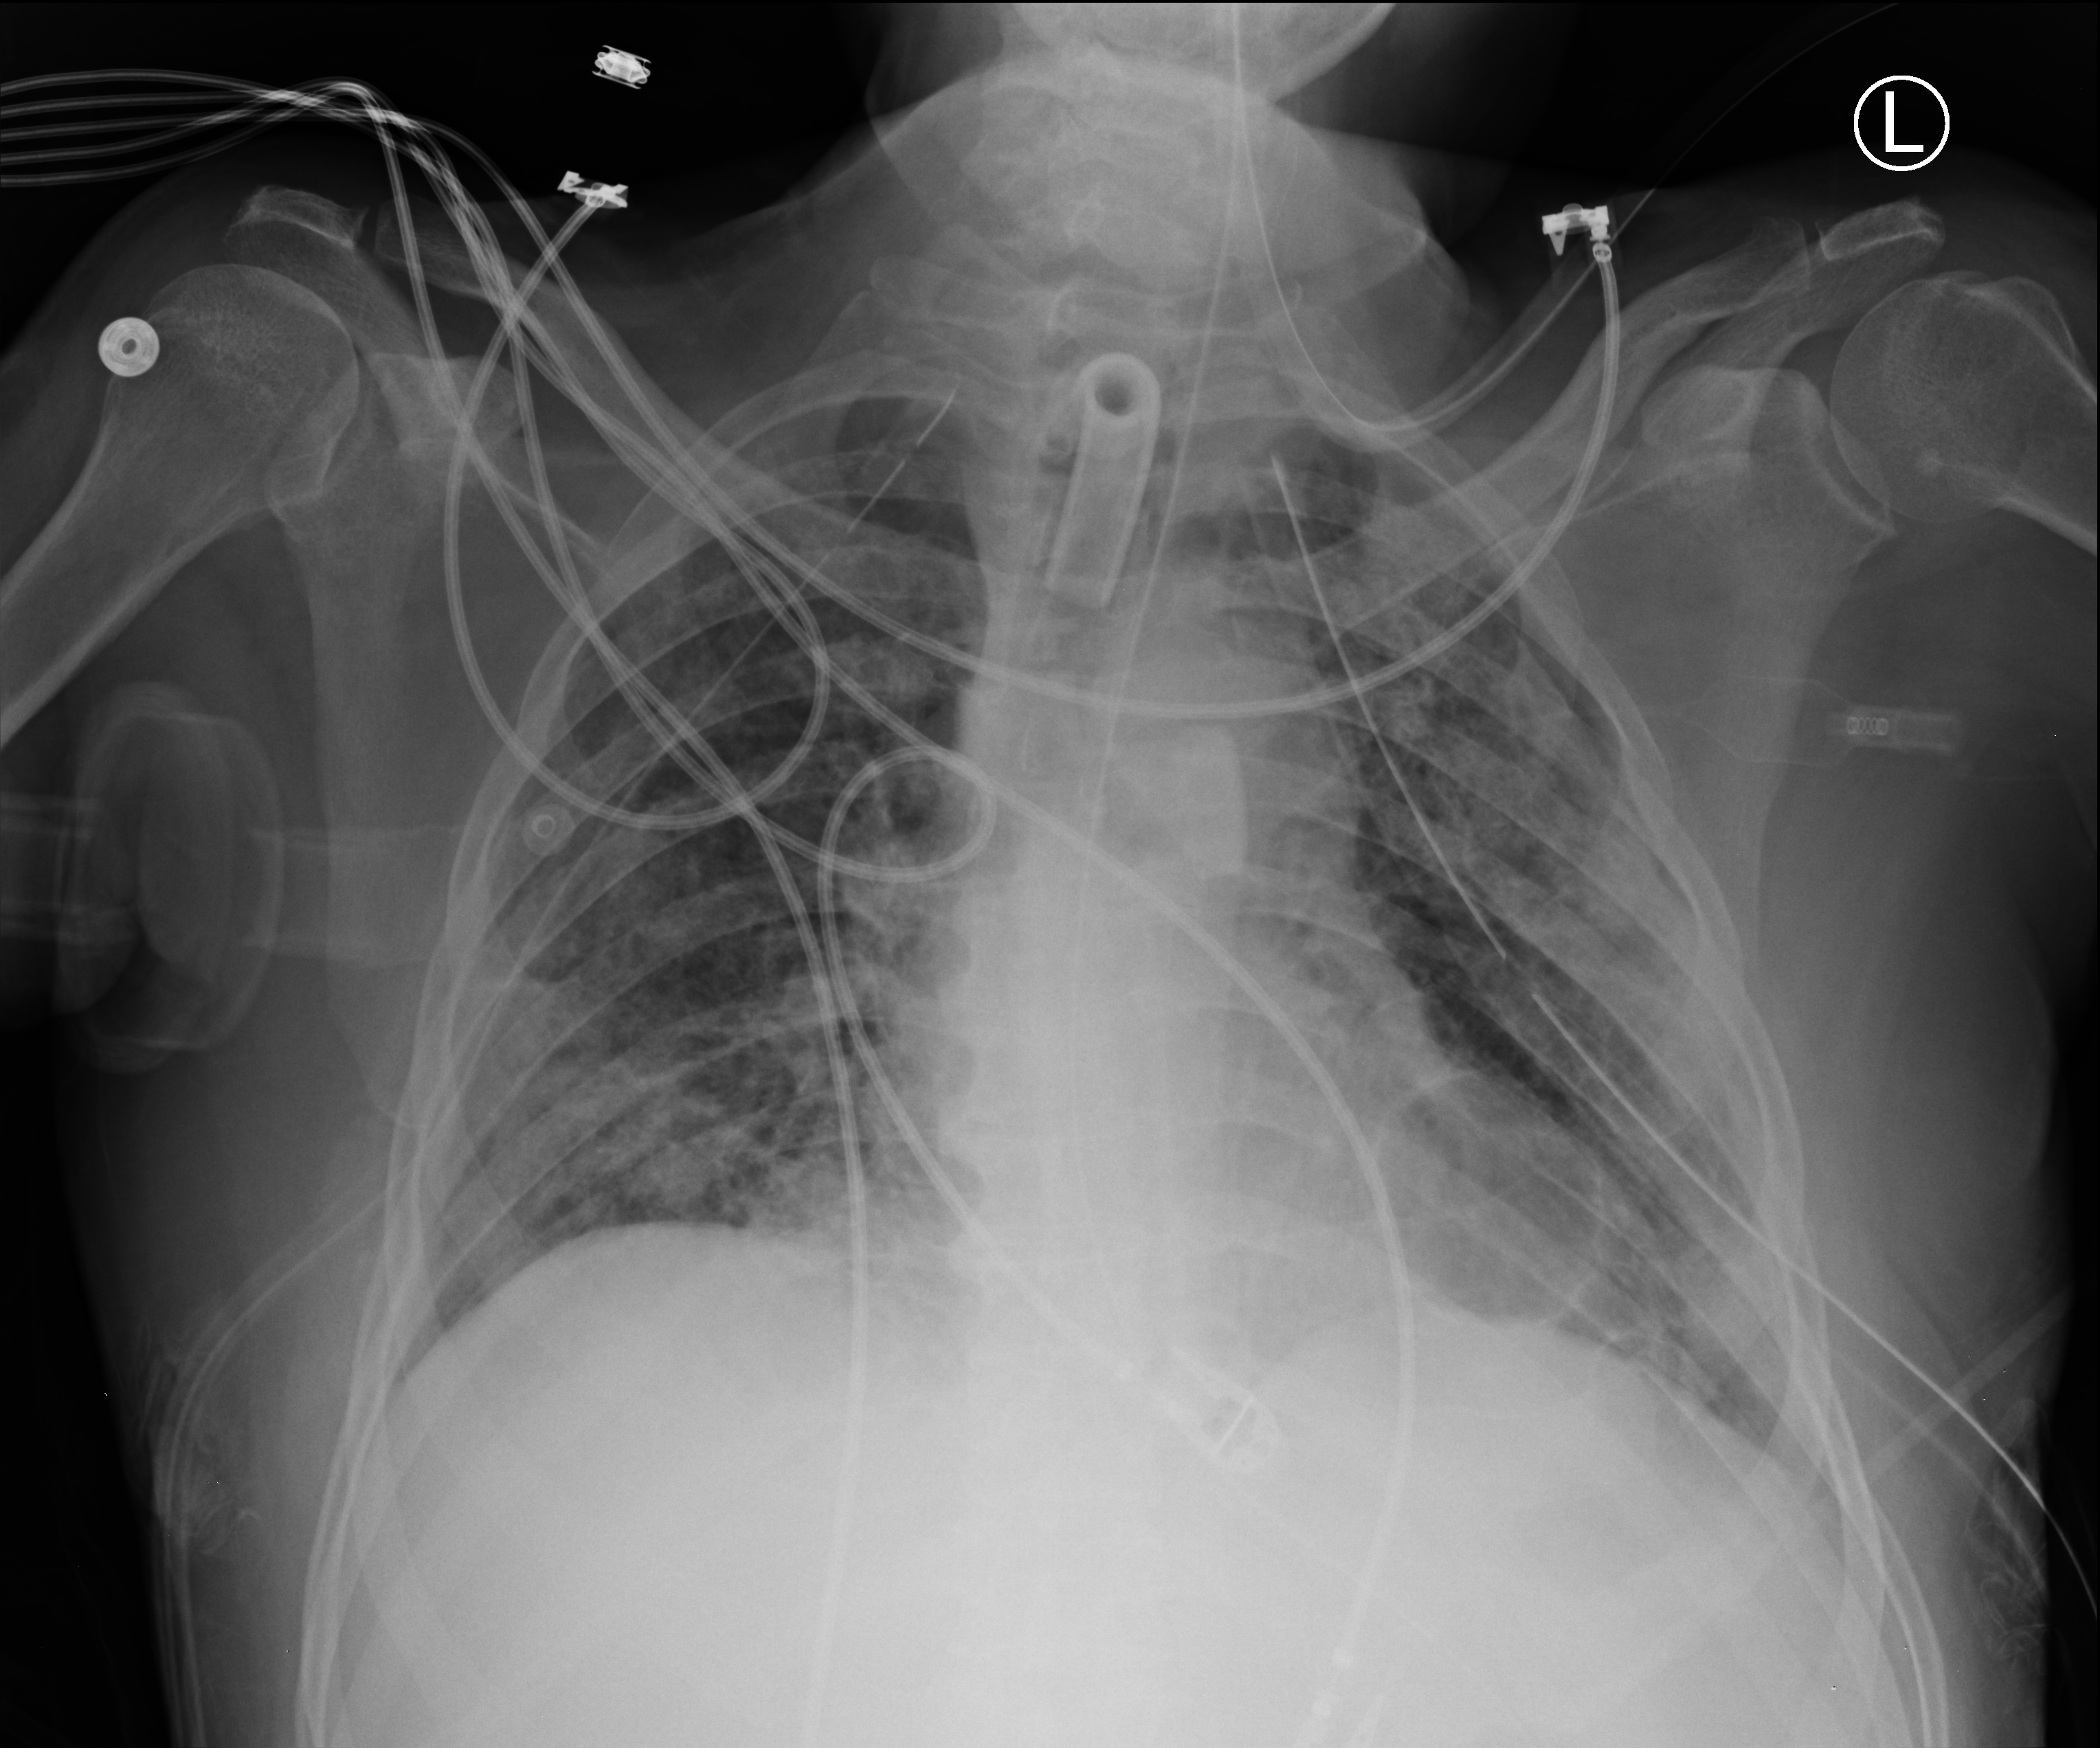
Bedside chest radiograph (computed radiography); anteroposterior (AP) projection. Patient hospitalised with COVID-19; male, aged 18–59 years.
From the hospital-stay record, not from the radiograph (when in the stay this image was taken is not recorded): mechanically ventilated during this hospital stay: yes; COPD (admission record): no; admitted to intensive care during this hospital stay: yes.